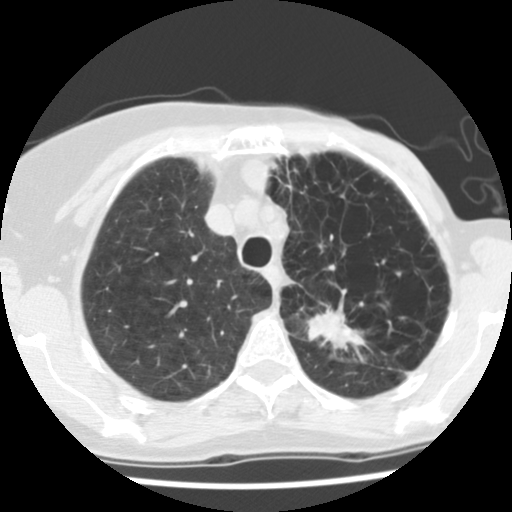
Low-dose screening chest CT, one axial slice; slice 101 of 128 in the series (ordered by position); 140 kVp; lung window (W 1500 / L -600 HU); 2.5 mm slice thickness; 512 × 512 image matrix.
Outlined on this slice (expert manual segmentation):
- lesion 1 (tumor, upper lobe of left lung): box from (x=307, y=309) to (x=367, y=355) px